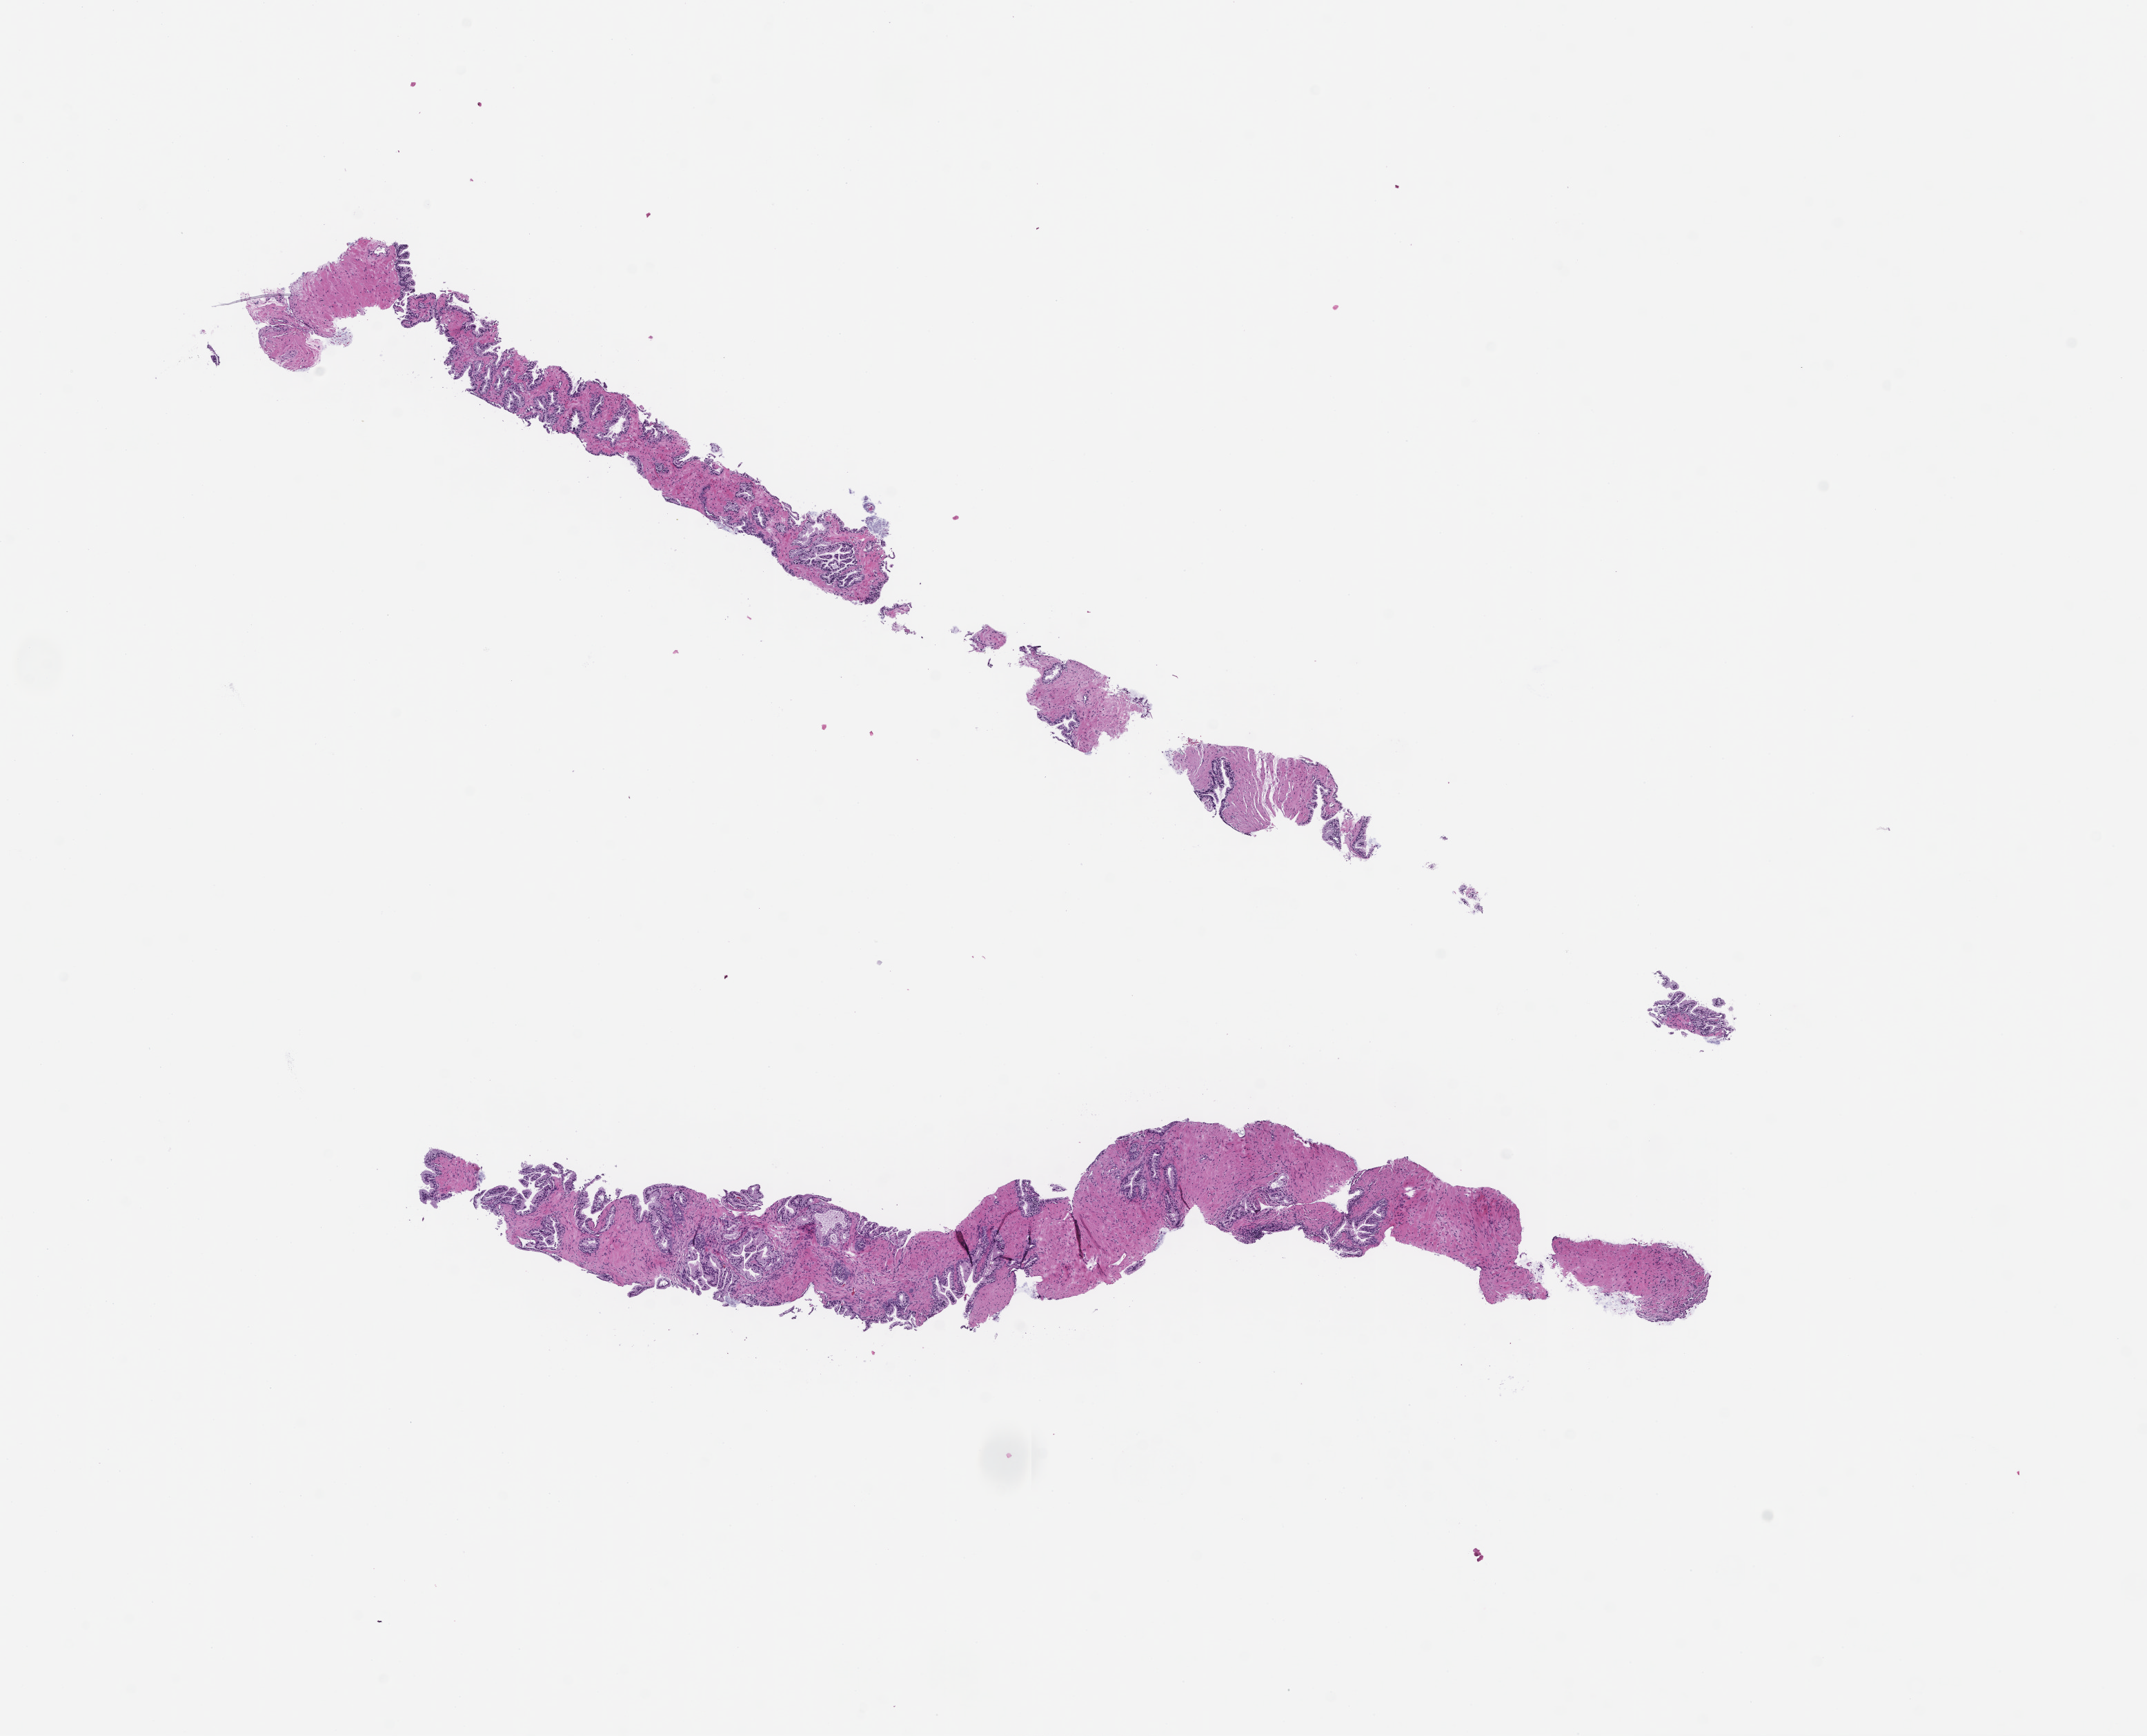
Whole-slide image, haematoxylin and eosin stain, whole scanned area (about 12.6 x 10.2 mm) shown as a low-resolution overview. Formalin-fixed, paraffin-embedded (FFPE) tissue. Site: prostate. Male patient.
* this section: primary tumour tissue
* diagnosis: Prostate Carcinoma